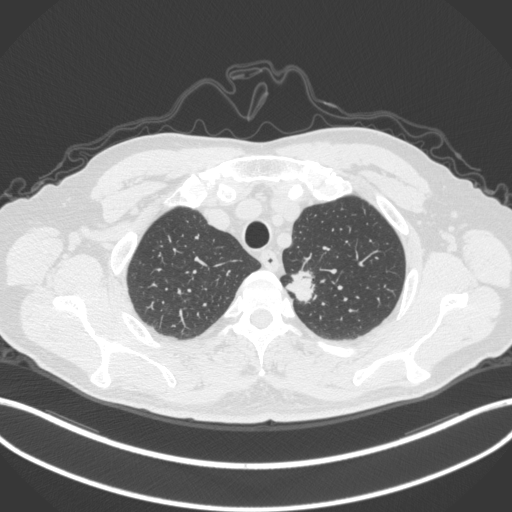
Chest CT, one axial slice. Position 319 of 382 along the scan axis. Reconstruction kernel B31f. Lung window (W 1500 / L -600 HU). 1 mm slice thickness. 512 × 512 image matrix, field of view 400 × 400 mm. Male patient, age 64 years. From the clinical record (not read from this slice): clinical TNM (as recorded): T1c N0 M0.
Structures marked on this image (bounding box drawn by a radiologist):
- lung tumour (recorded histology: adenocarcinoma): bounding box [x1, y1, x2, y2] px = [282, 260, 323, 307]